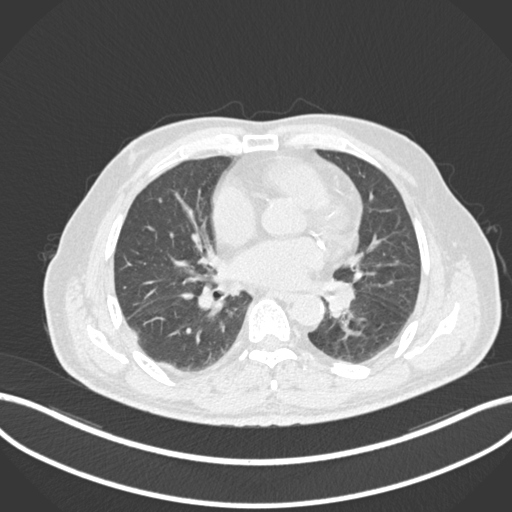
Chest CT, one axial slice; position 63 of 161 along the scan axis; reconstruction kernel B30f; 120 kVp; lung window (W 1500 / L -600 HU); 1 mm slice thickness; 512 × 512 image matrix. Male patient, age 71 years. Case-level facts recorded for this patient, not image findings: clinical TNM (as recorded): T1b N0 M0.
Structures marked on this image (rectangle marked by the reading radiologist):
- lung tumour (recorded histology: squamous cell carcinoma): bounding box [x1, y1, x2, y2] px = [326, 279, 359, 321]